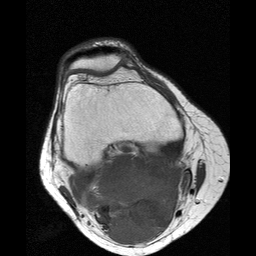
MRI of an extremity soft-tissue mass, one axial slice. Slice 12 of 25 in the series (ordered by position). 256 × 256 image matrix. Female patient. Case-level facts recorded for this patient, not image findings: histological type: liposarcoma; site of the primary tumour: right thigh.
Structures marked on this image (manually delineated by an expert):
- gross tumour volume (mass): bounding box [x1, y1, x2, y2] px = [84, 154, 186, 245]